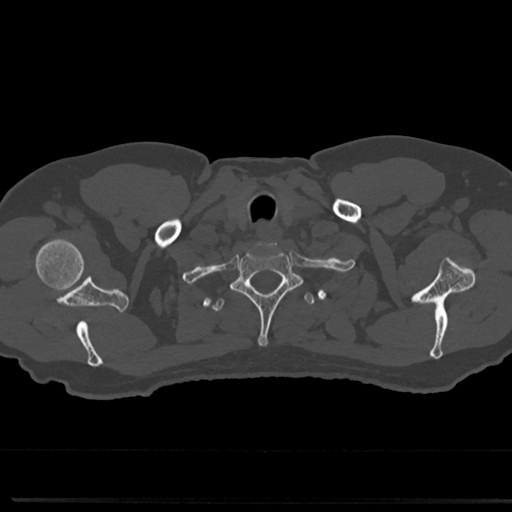
CT including the spine, one axial slice. Slice 670 of 817 in the series (ordered by position). Reconstruction kernel Br40s/3. 120 kVp. Bone window (W 1800 / L 400 HU). 0.5 mm slice thickness. 512 × 512 image matrix, field of view 355 × 355 mm. Male patient, age 61 years. From the clinical record (not read from this slice): primary cancer: prostate.
Structures marked on this image (semi-automatic segmentation, software-assisted and operator-edited):
- T1 vertebra: bounding box <233,247,299,345> (left, top, right, bottom; pixels)
- T2 vertebra: <212,291,315,315>